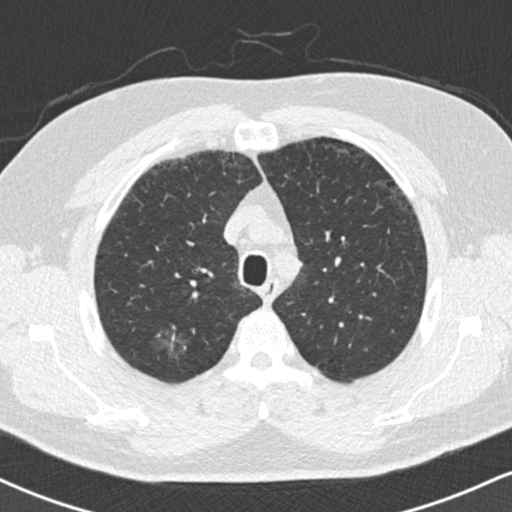
Axial slice from a low-dose chest CT screening exam, second screening round (one year after baseline), lung window (W 1500 / L -600 HU), 2 mm slice thickness, standard (soft-tissue) reconstruction kernel (B30f). Male, age 59 years at enrolment. Current smoker at enrolment.
• Expert-annotated lung lesion, bounding box (x1, y1, x2, y2) in pixels: (152, 311, 204, 364).
• The exam's reader record, not a measurement of the box and not confirmed to be the same lesion: non-calcified nodule or mass ≥4 mm, right upper lobe, 18 × 16 mm, ground glass attenuation, pre-existing on the prior screen: yes.
• Official screen result: positive, no significant change: stable abnormalities potentially related to lung cancer, unchanged since the prior screening exam.
• Later outcome: lung cancer diagnosed 60 days after this screen — bronchiolo-alveolar adenocarcinoma, NOS, right lower lobe, stage IA (AJCC 6th edition), 15 mm at pathology.